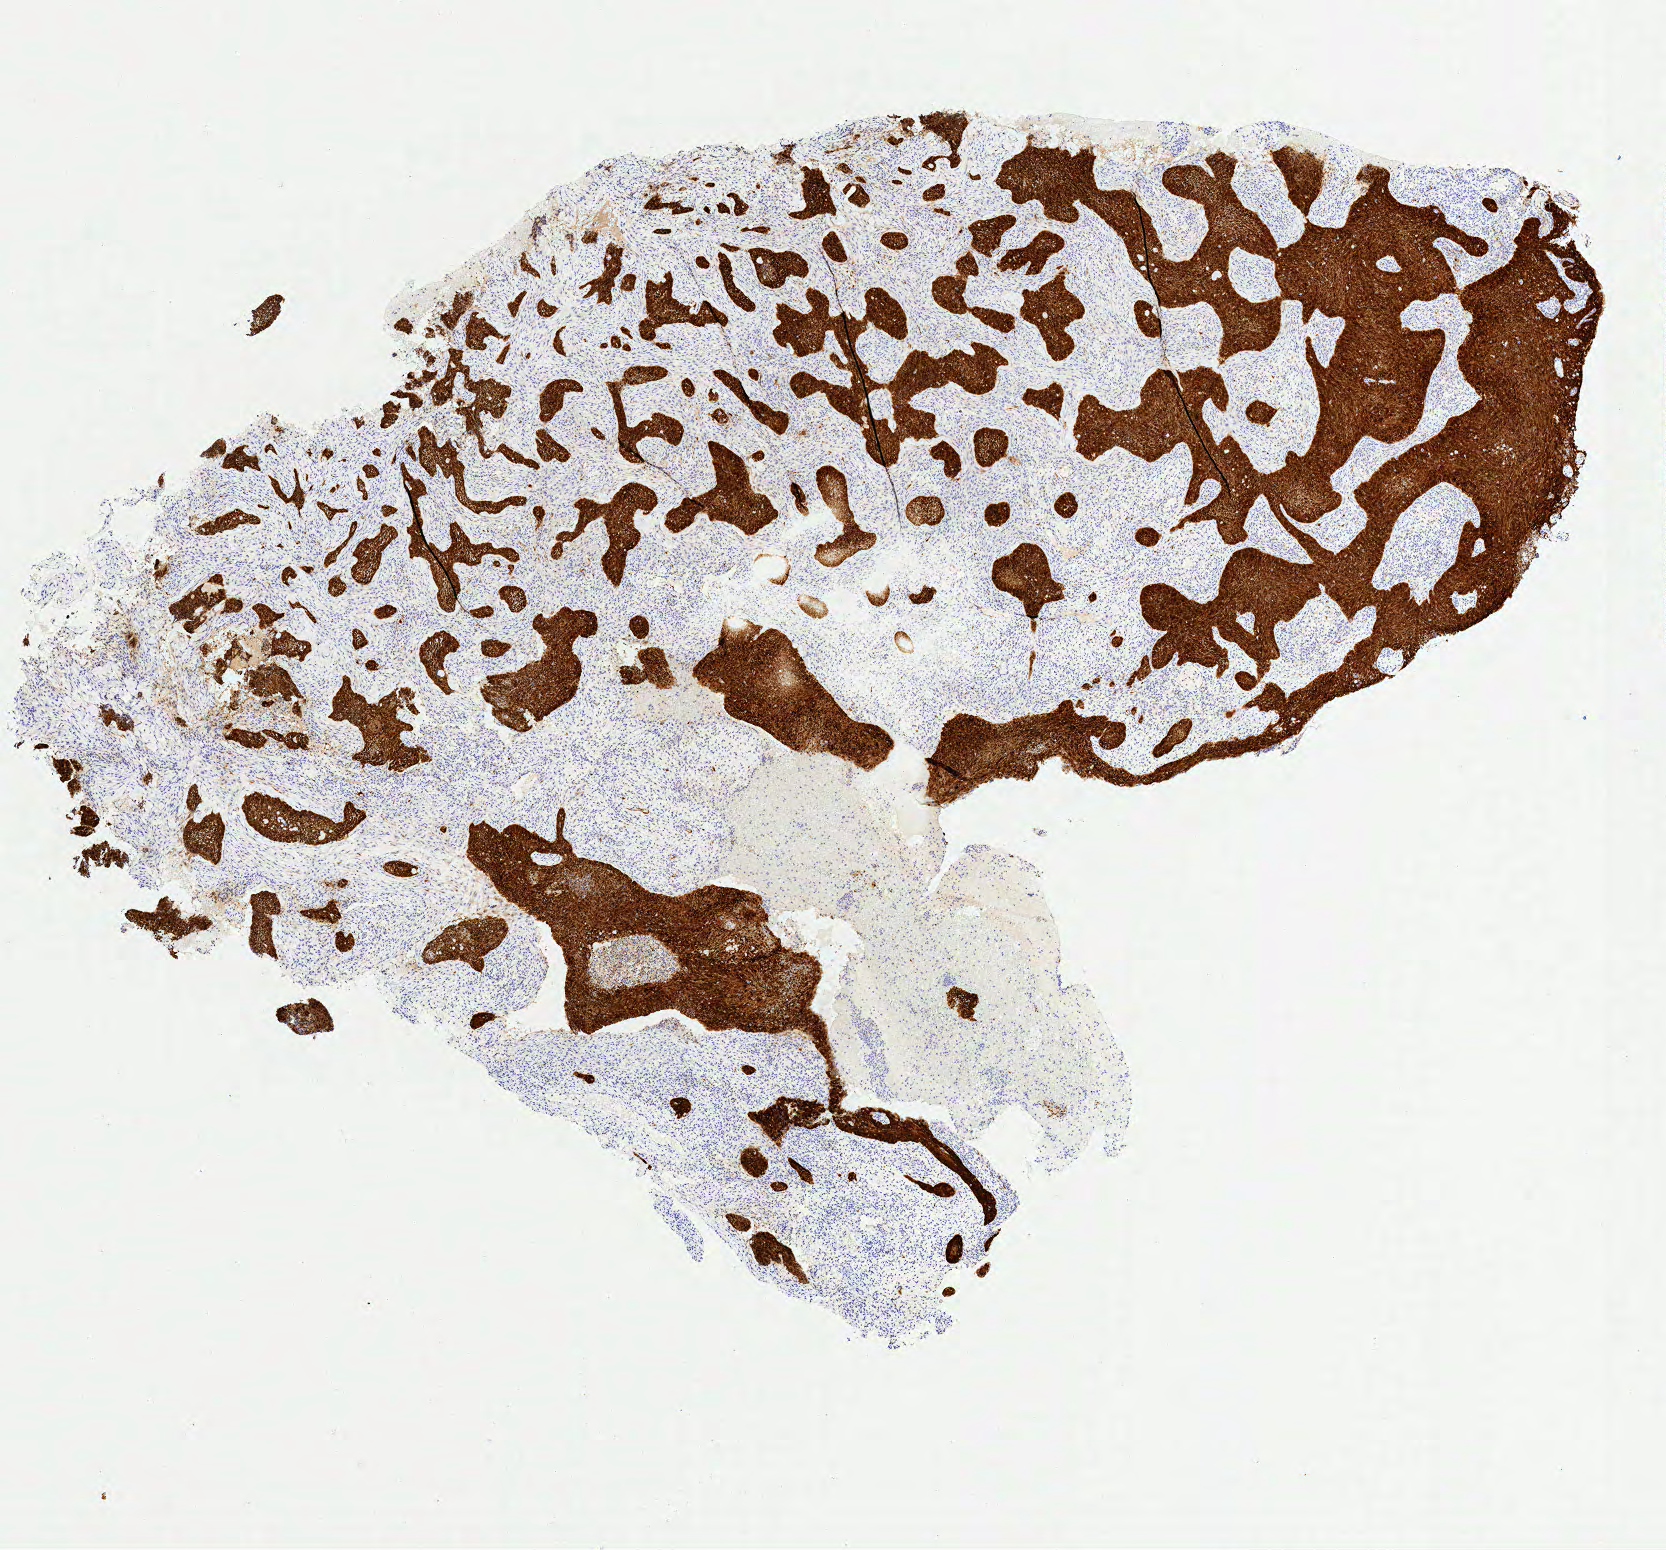
Whole-slide image, immunohistochemical stain for p16 (p16INK4a) — whole scanned area (about 6.6 x 6.1 mm) shown as a low-resolution overview, specimen: tumor tissue, site: cervix. Female patient, 44 years old.
Histologic diagnosis: Squamous cell carcinoma, large cell, nonkeratinizing, NOS.